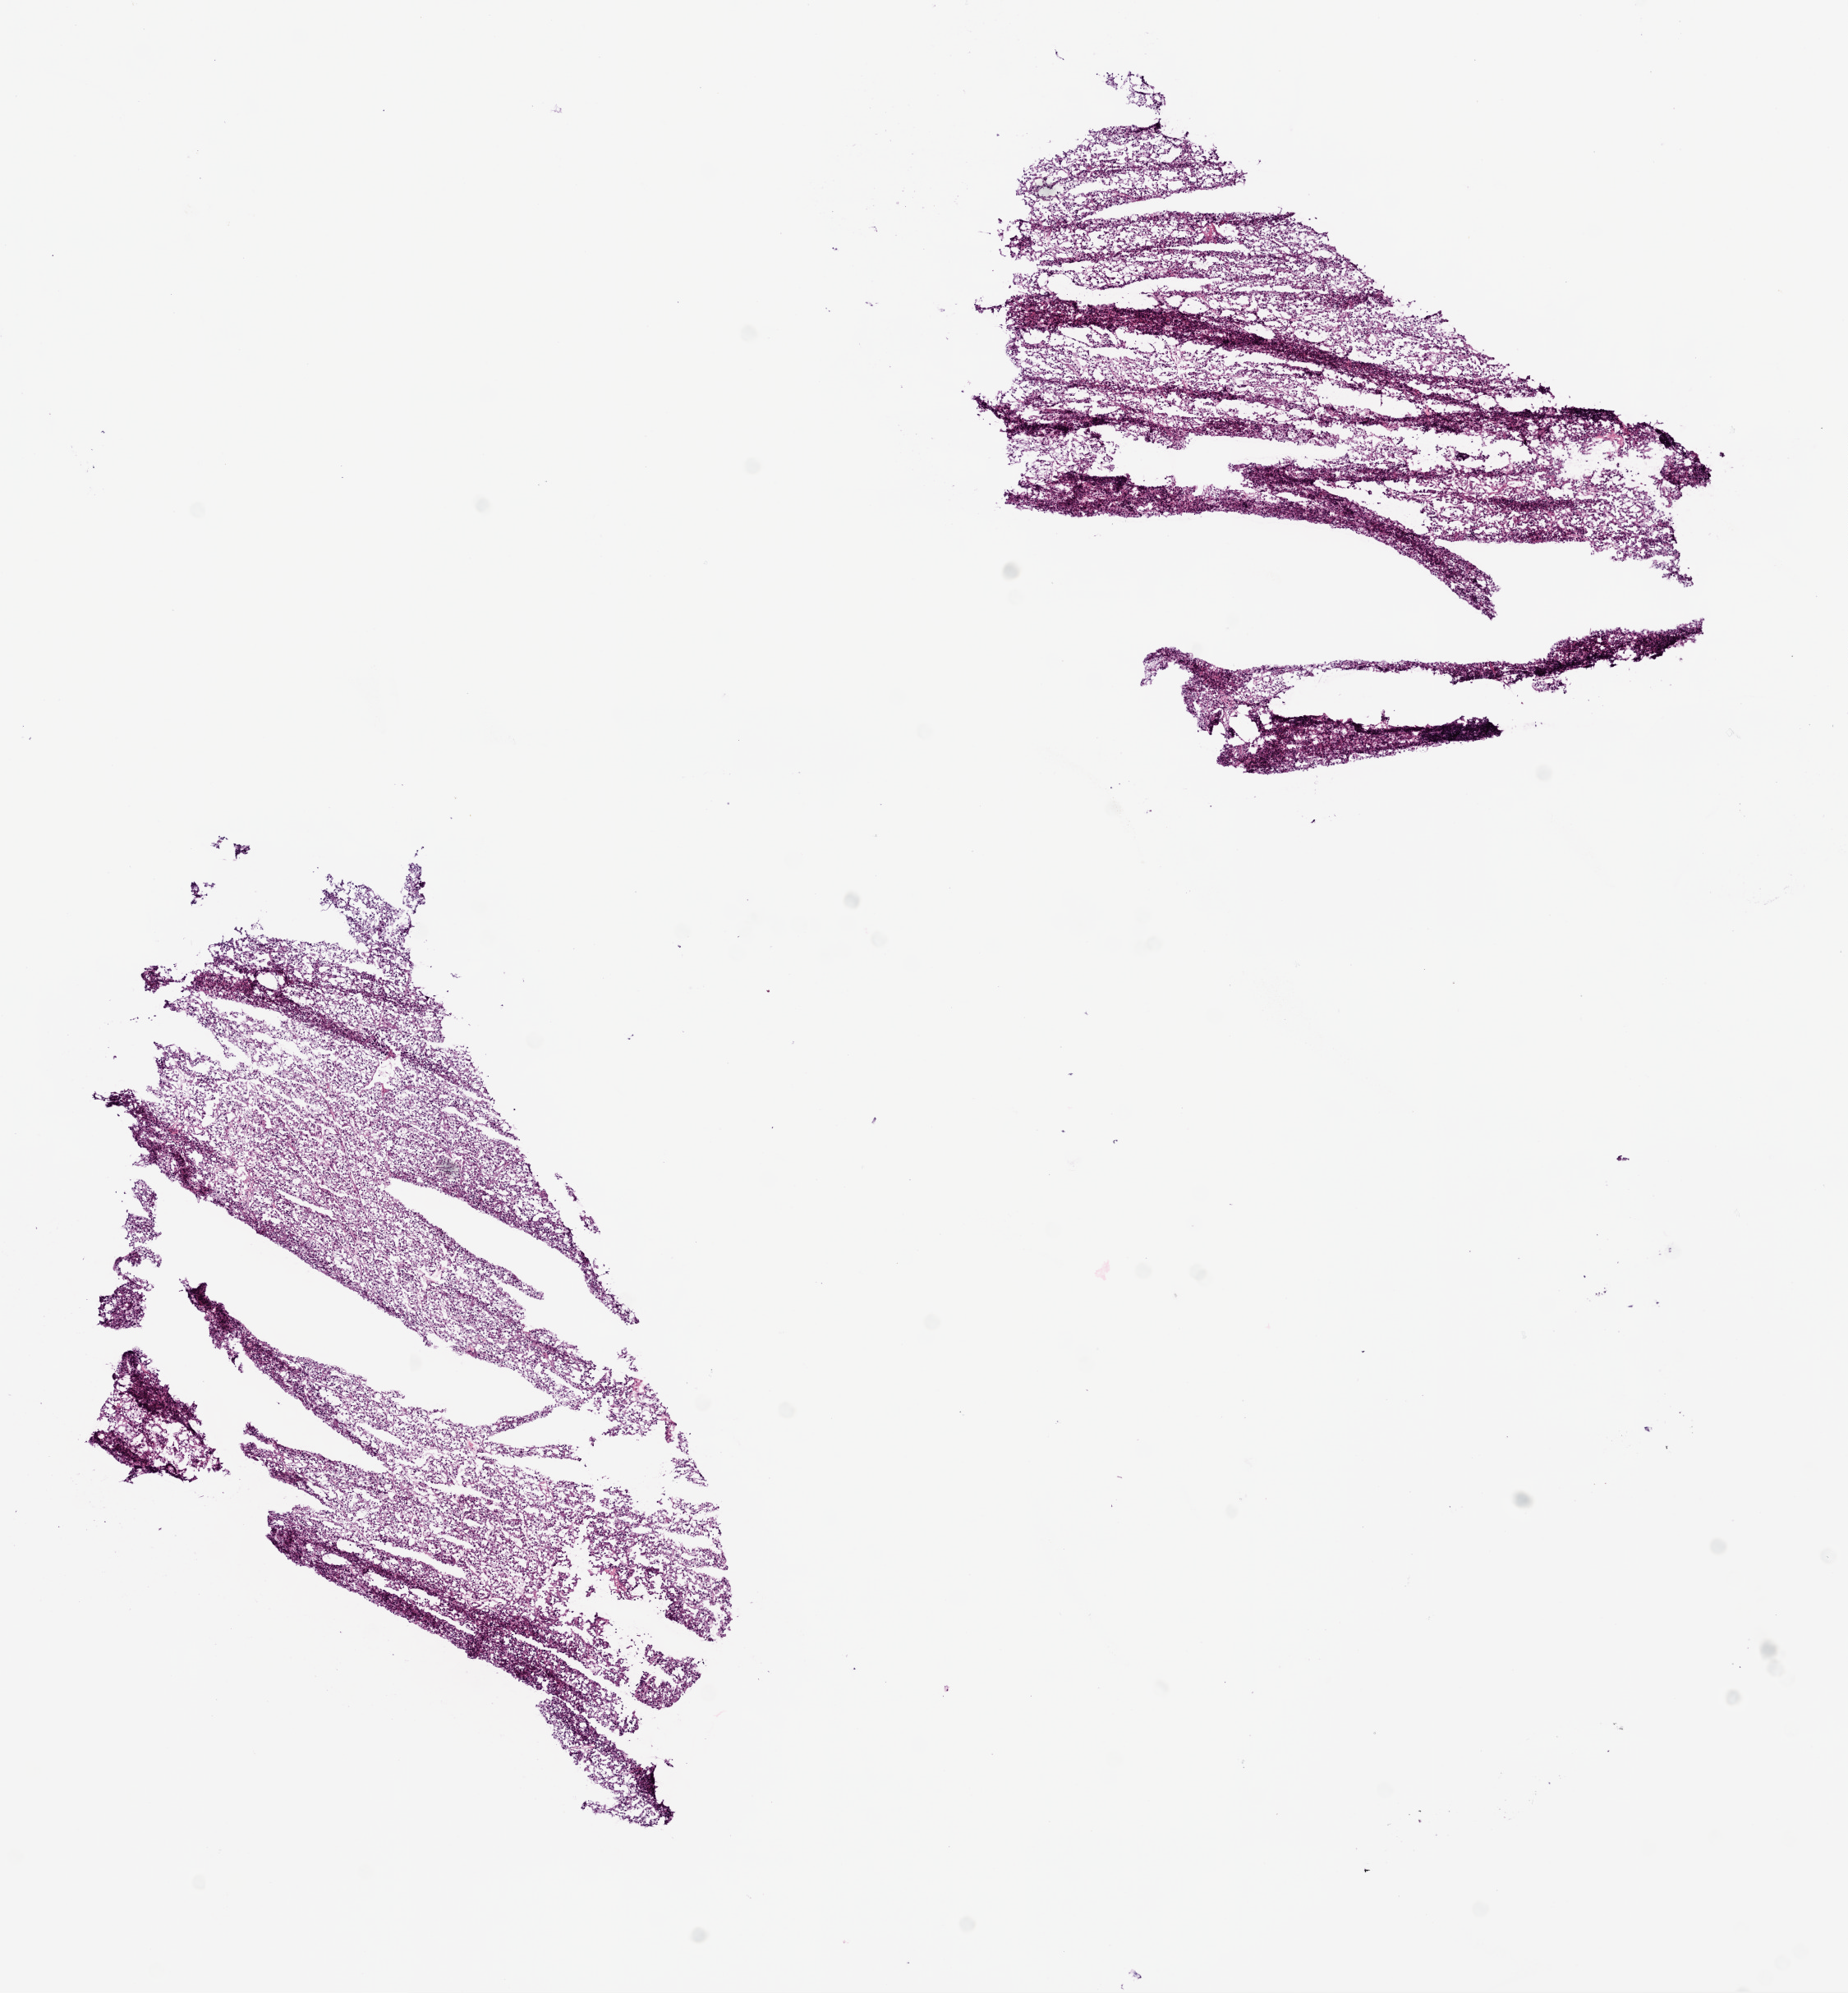
Whole-slide histology image, H&E, low-resolution overview of the scanned area, about 9.0 x 9.7 mm; frozen section from the bottom of the tissue portion; primary tumour sample from the kidney. Female, age 46 years at initial diagnosis. Histologic grade: G2 (moderately differentiated). Slide review estimates, as recorded: tumour cells 95%, tumour nuclei 85%, normal cells 0%, stromal cells 5%, necrosis 0%.
• histologic diagnosis: Clear cell adenocarcinoma, NOS
• TNM: T1a N0 M0
• AJCC pathologic stage: I